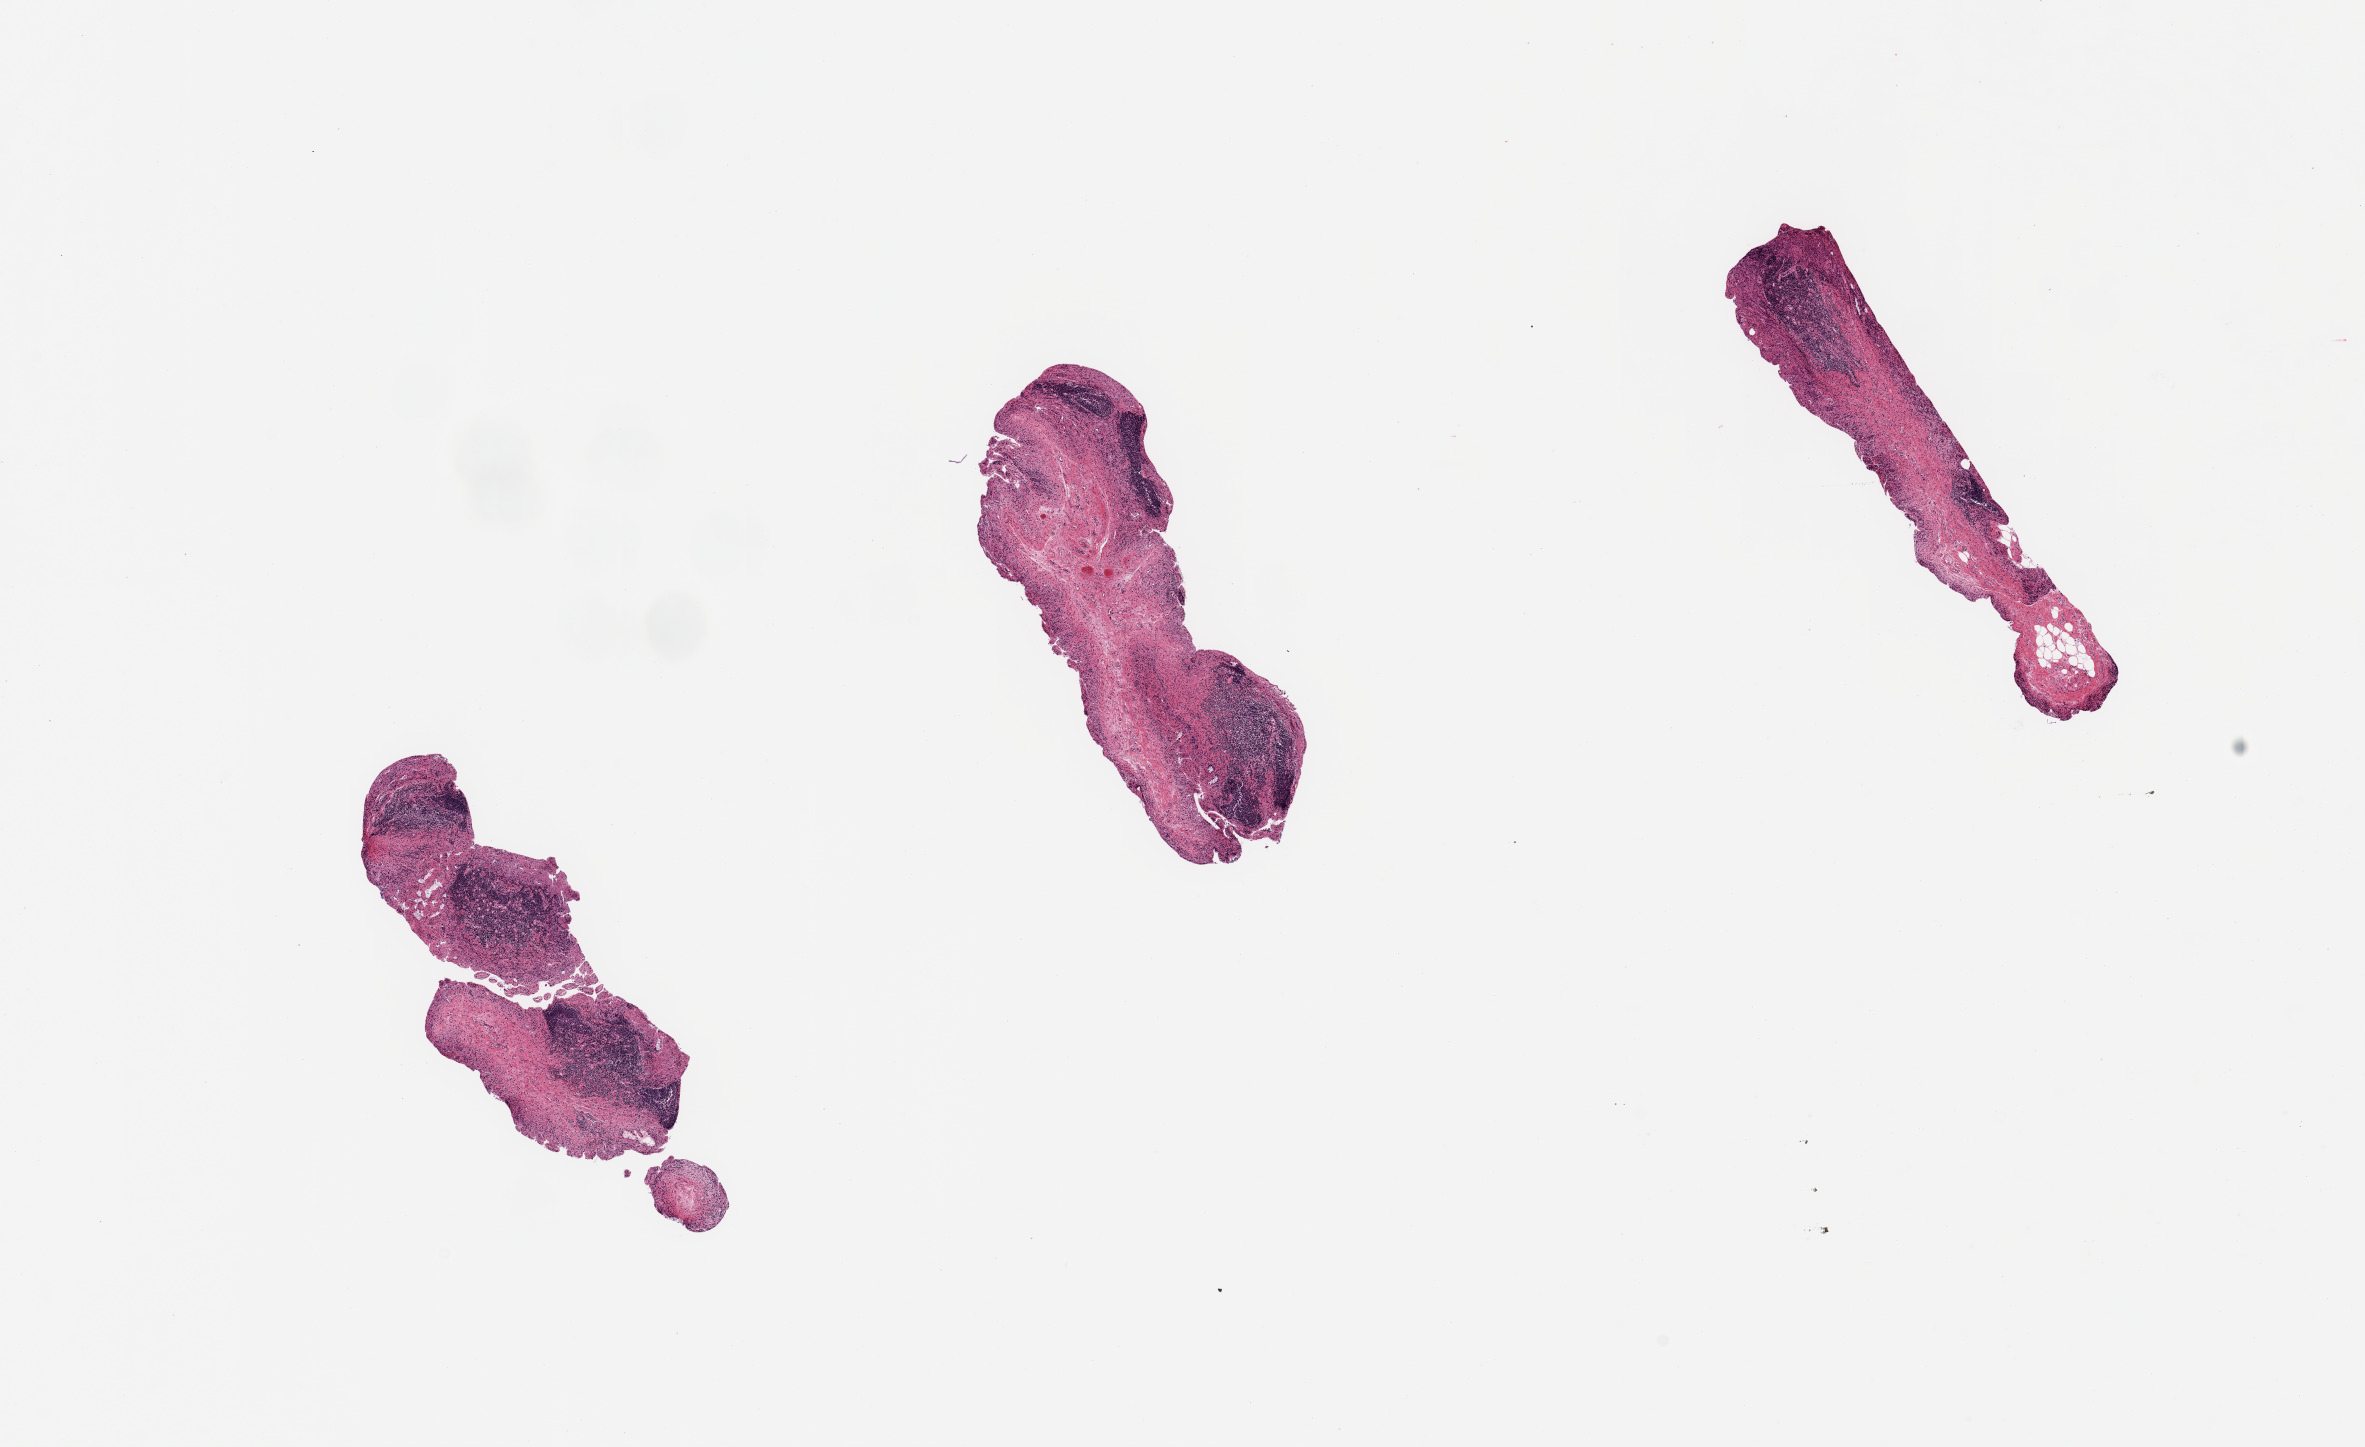
Digitized haematoxylin and eosin-stained section, whole scanned area (about 18.7 x 11.4 mm) shown as a low-resolution overview, PAXgene-fixed paraffin-embedded (PFPE) section, target tissue: ileum, tissue donor sample. Donor sex: male.
• reviewer comment on this tissue sample: 3 pieces; ~30% target lymphoid aggregates